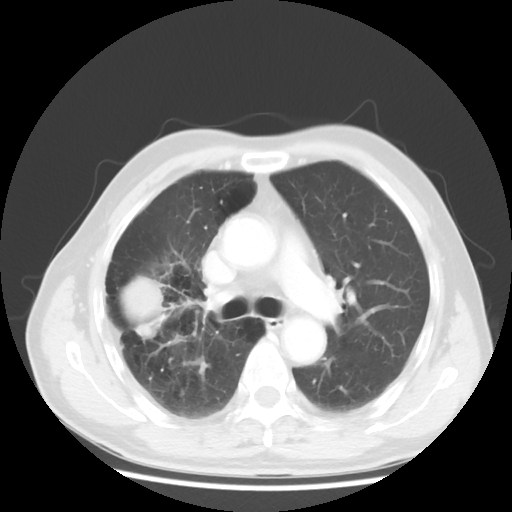
Chest CT, one axial slice. Position 31 of 50 along the scan axis. 120 kVp. Lung window (W 1500 / L -600 HU). 5 mm slice thickness. 512 × 512 image matrix, field of view 360 × 360 mm. Male patient, age 69 years. Case-level facts recorded for this patient, not image findings: clinical TNM (as recorded): T3 N0 M0; histopathological grade: G3.
Outlined on this slice (bounding box drawn by a radiologist):
- lung tumour (recorded histology: adenocarcinoma): box from (x=115, y=275) to (x=173, y=331) px